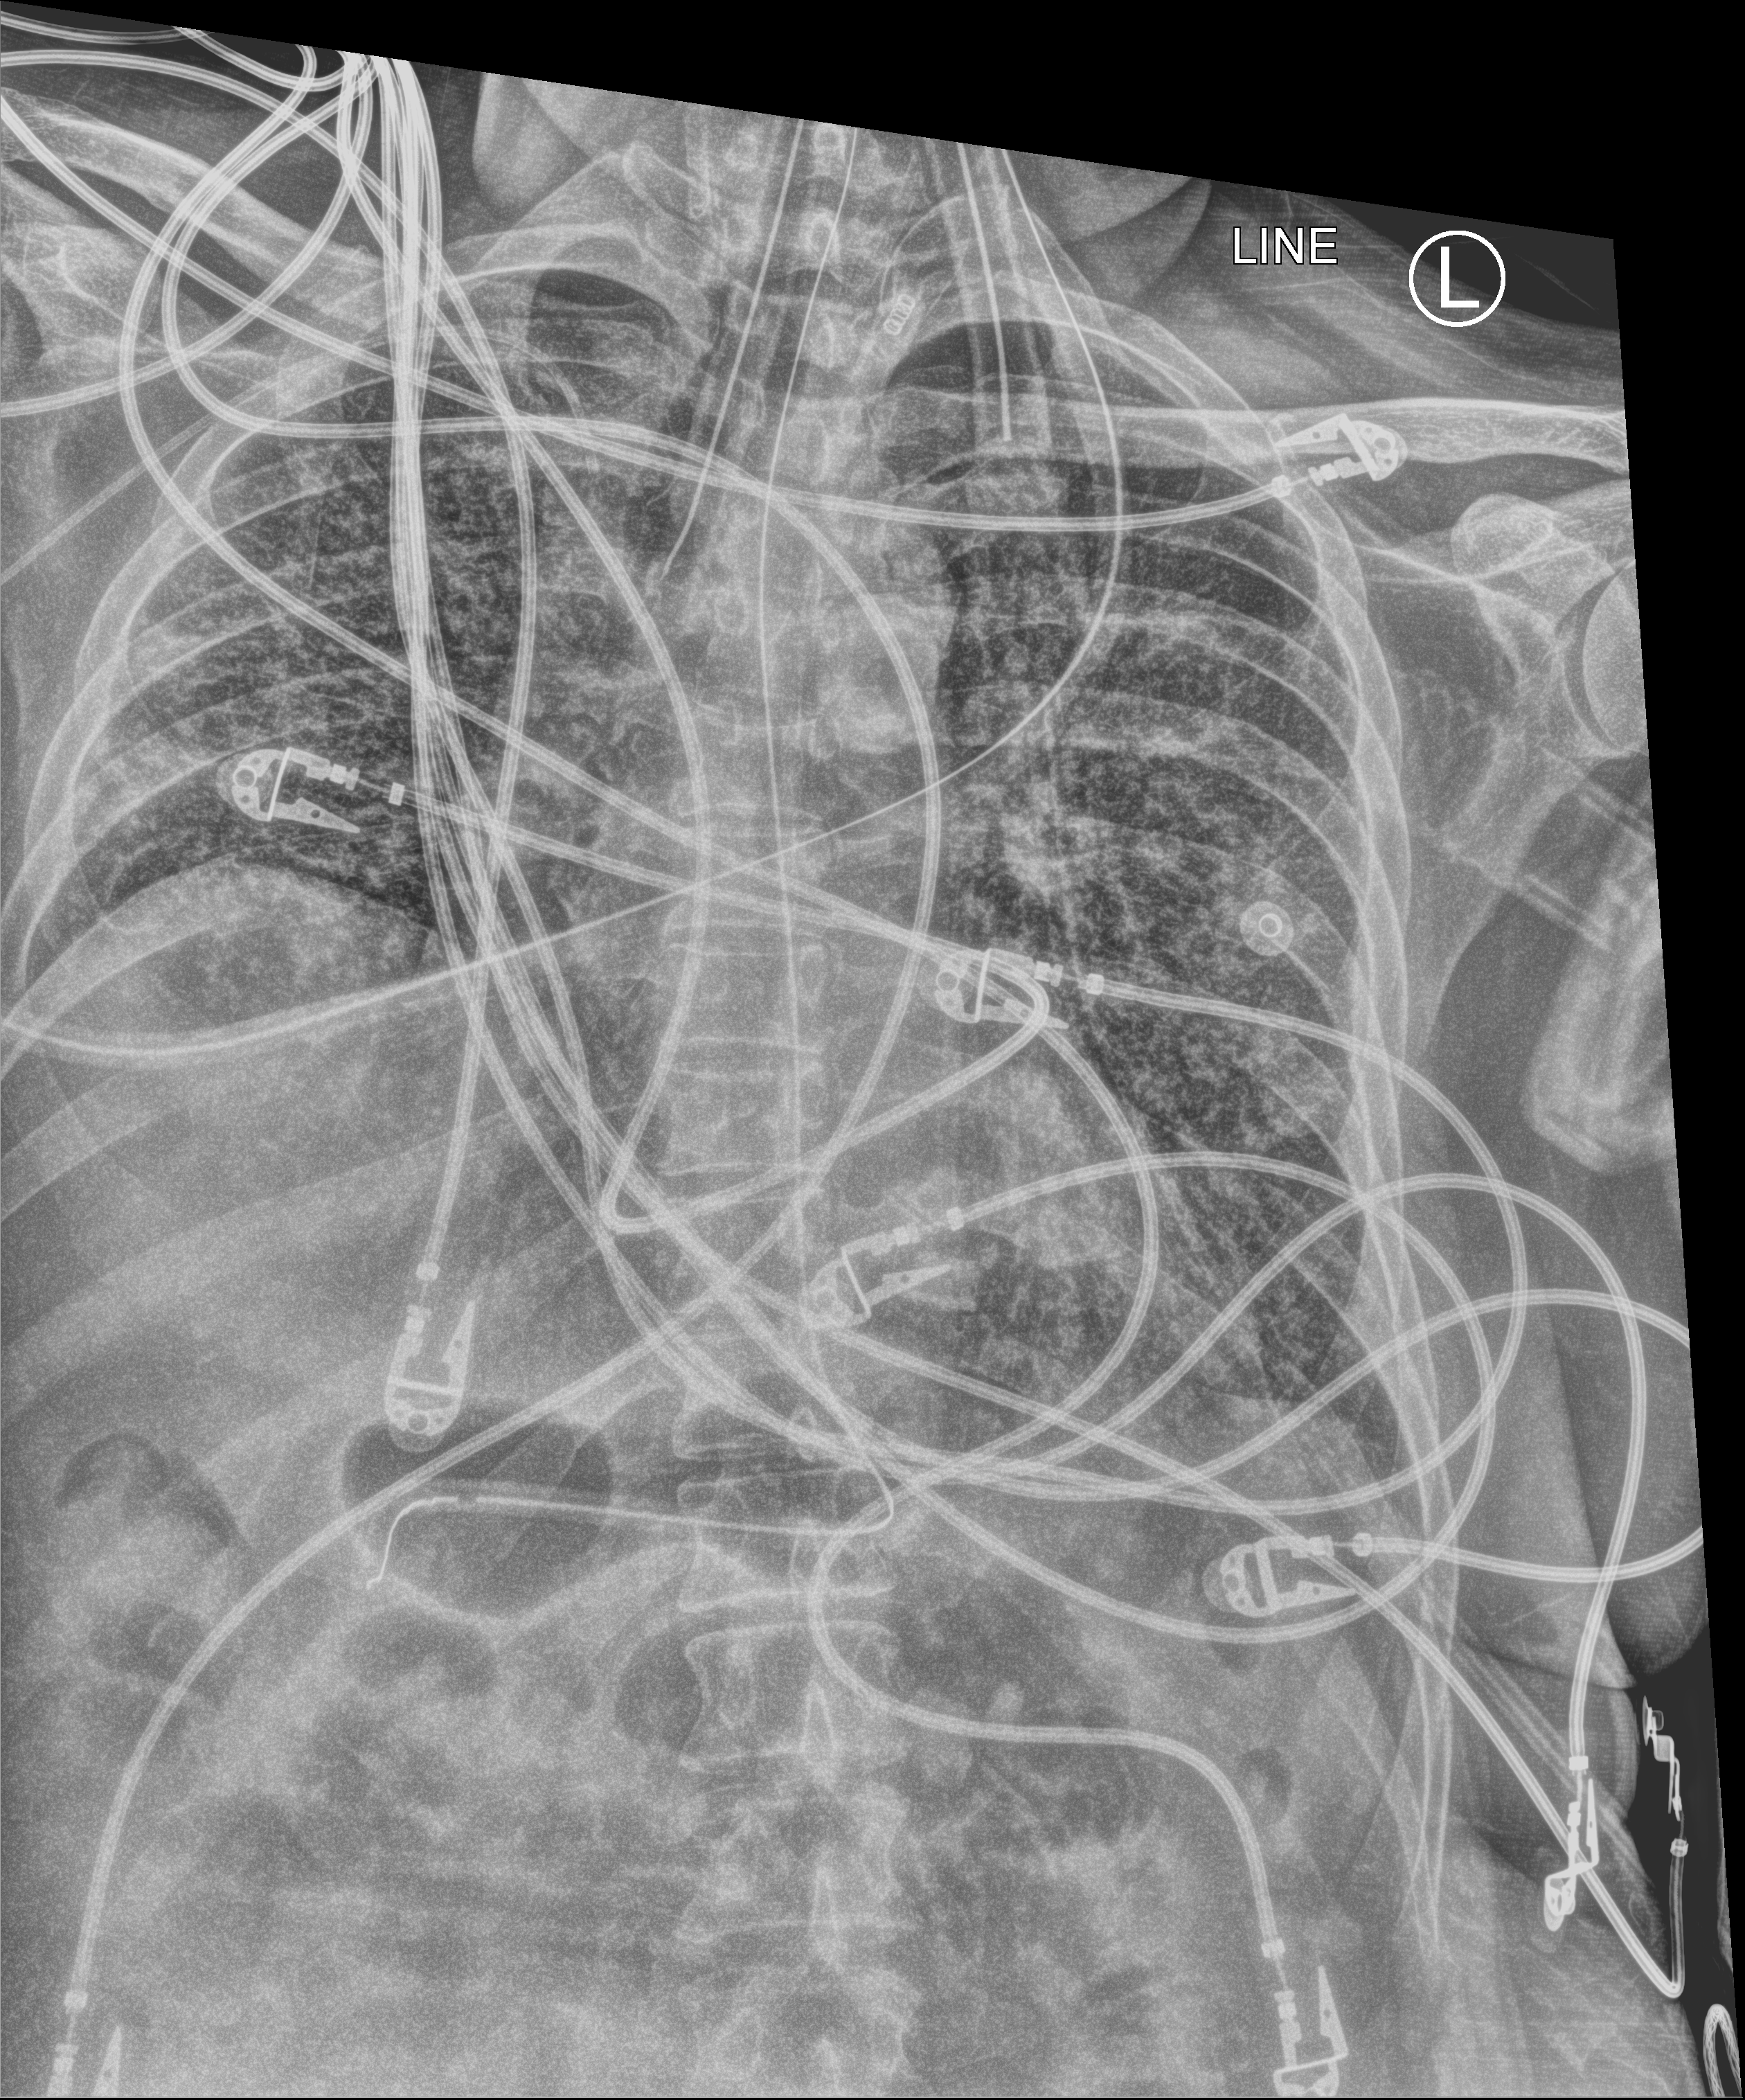
Portable chest radiograph; anteroposterior (AP) projection. Male patient hospitalised with COVID-19, age 18–59 years.
From the hospital-stay record, not from the radiograph (when in the stay this image was taken is not recorded): admitted to intensive care during this hospital stay: yes.